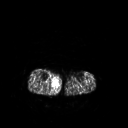
FDG PET of an extremity soft-tissue mass (from a PET/CT study), one axial slice; position 125 of 267 along the scan axis; 3.27 mm slice thickness; 128 × 128 image matrix, field of view 500 × 500 mm. Male patient, age 69 years. Case-level facts recorded for this patient, not image findings: histological type: pleiomorphic liposarcoma; grade: high; site of the primary tumour: right calf.
Annotated regions visible in this slice (expert contour drawn on MRI and transferred to this co-registered scan by the dataset authors):
- gross tumour volume including surrounding oedema: box from (x=51, y=78) to (x=59, y=92) px
- gross tumour volume (mass): (x=52, y=80)–(x=58, y=86)